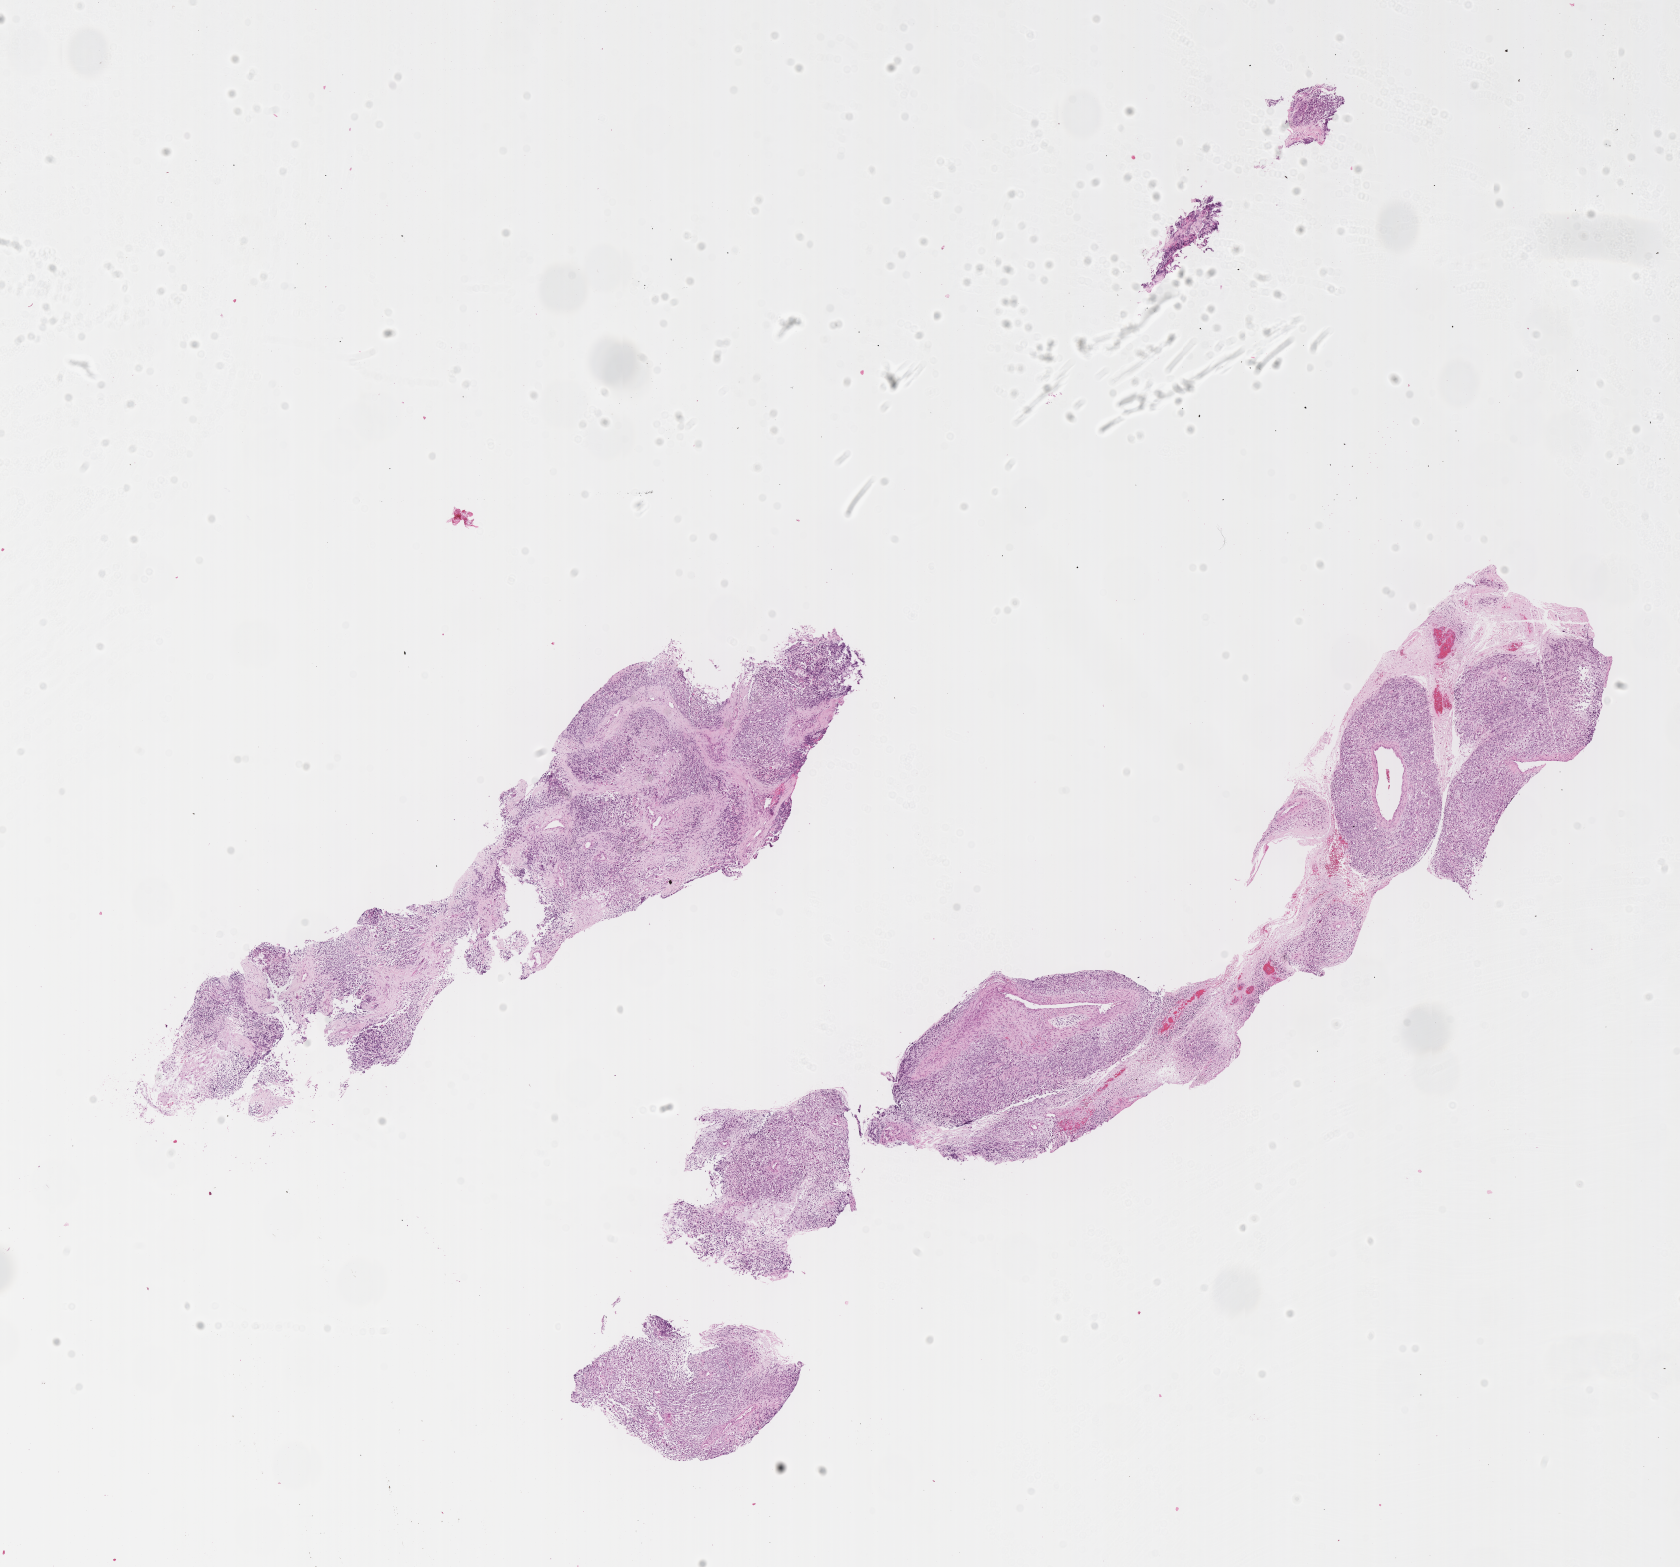
Digitized hematoxylin and eosin (H&E)-stained section of tumor tissue — a low-resolution overview of the entire scanned area, about 13.6 x 12.7 mm. FFPE section. Sample anatomic site: prostate. Male patient, age at diagnosis 17.3 years.
Diagnosis: rhabdomyosarcoma; histological classification: embryonal rhabdomyosarcoma.